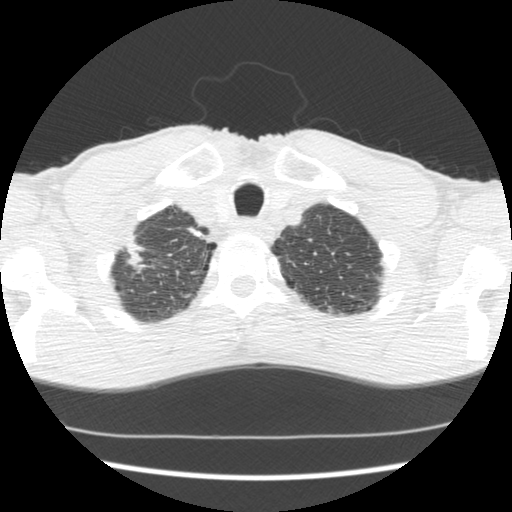
Axial slice from a low-dose chest CT screening exam; first (baseline) screen; lung window (W 1500 / L -600 HU); 2.5 mm slice thickness; slice 27 of 197 in the series. Male, age 62 years at enrolment. Current smoker at enrolment.
• Expert reader's lesion annotation, bounding box <104,226,154,274> (left, top, right, bottom; pixels).
• No non-calcified nodule or mass ≥4 mm was recorded by the screening reader at this exam.
• Official screen result: negative screen, significant abnormalities not suspicious for lung cancer.
• Lung cancer was diagnosed 640 days after this screen: adenocarcinoma, NOS, right upper lobe, poorly differentiated (G3), stage IIA (AJCC 6th edition), 22 mm at pathology.